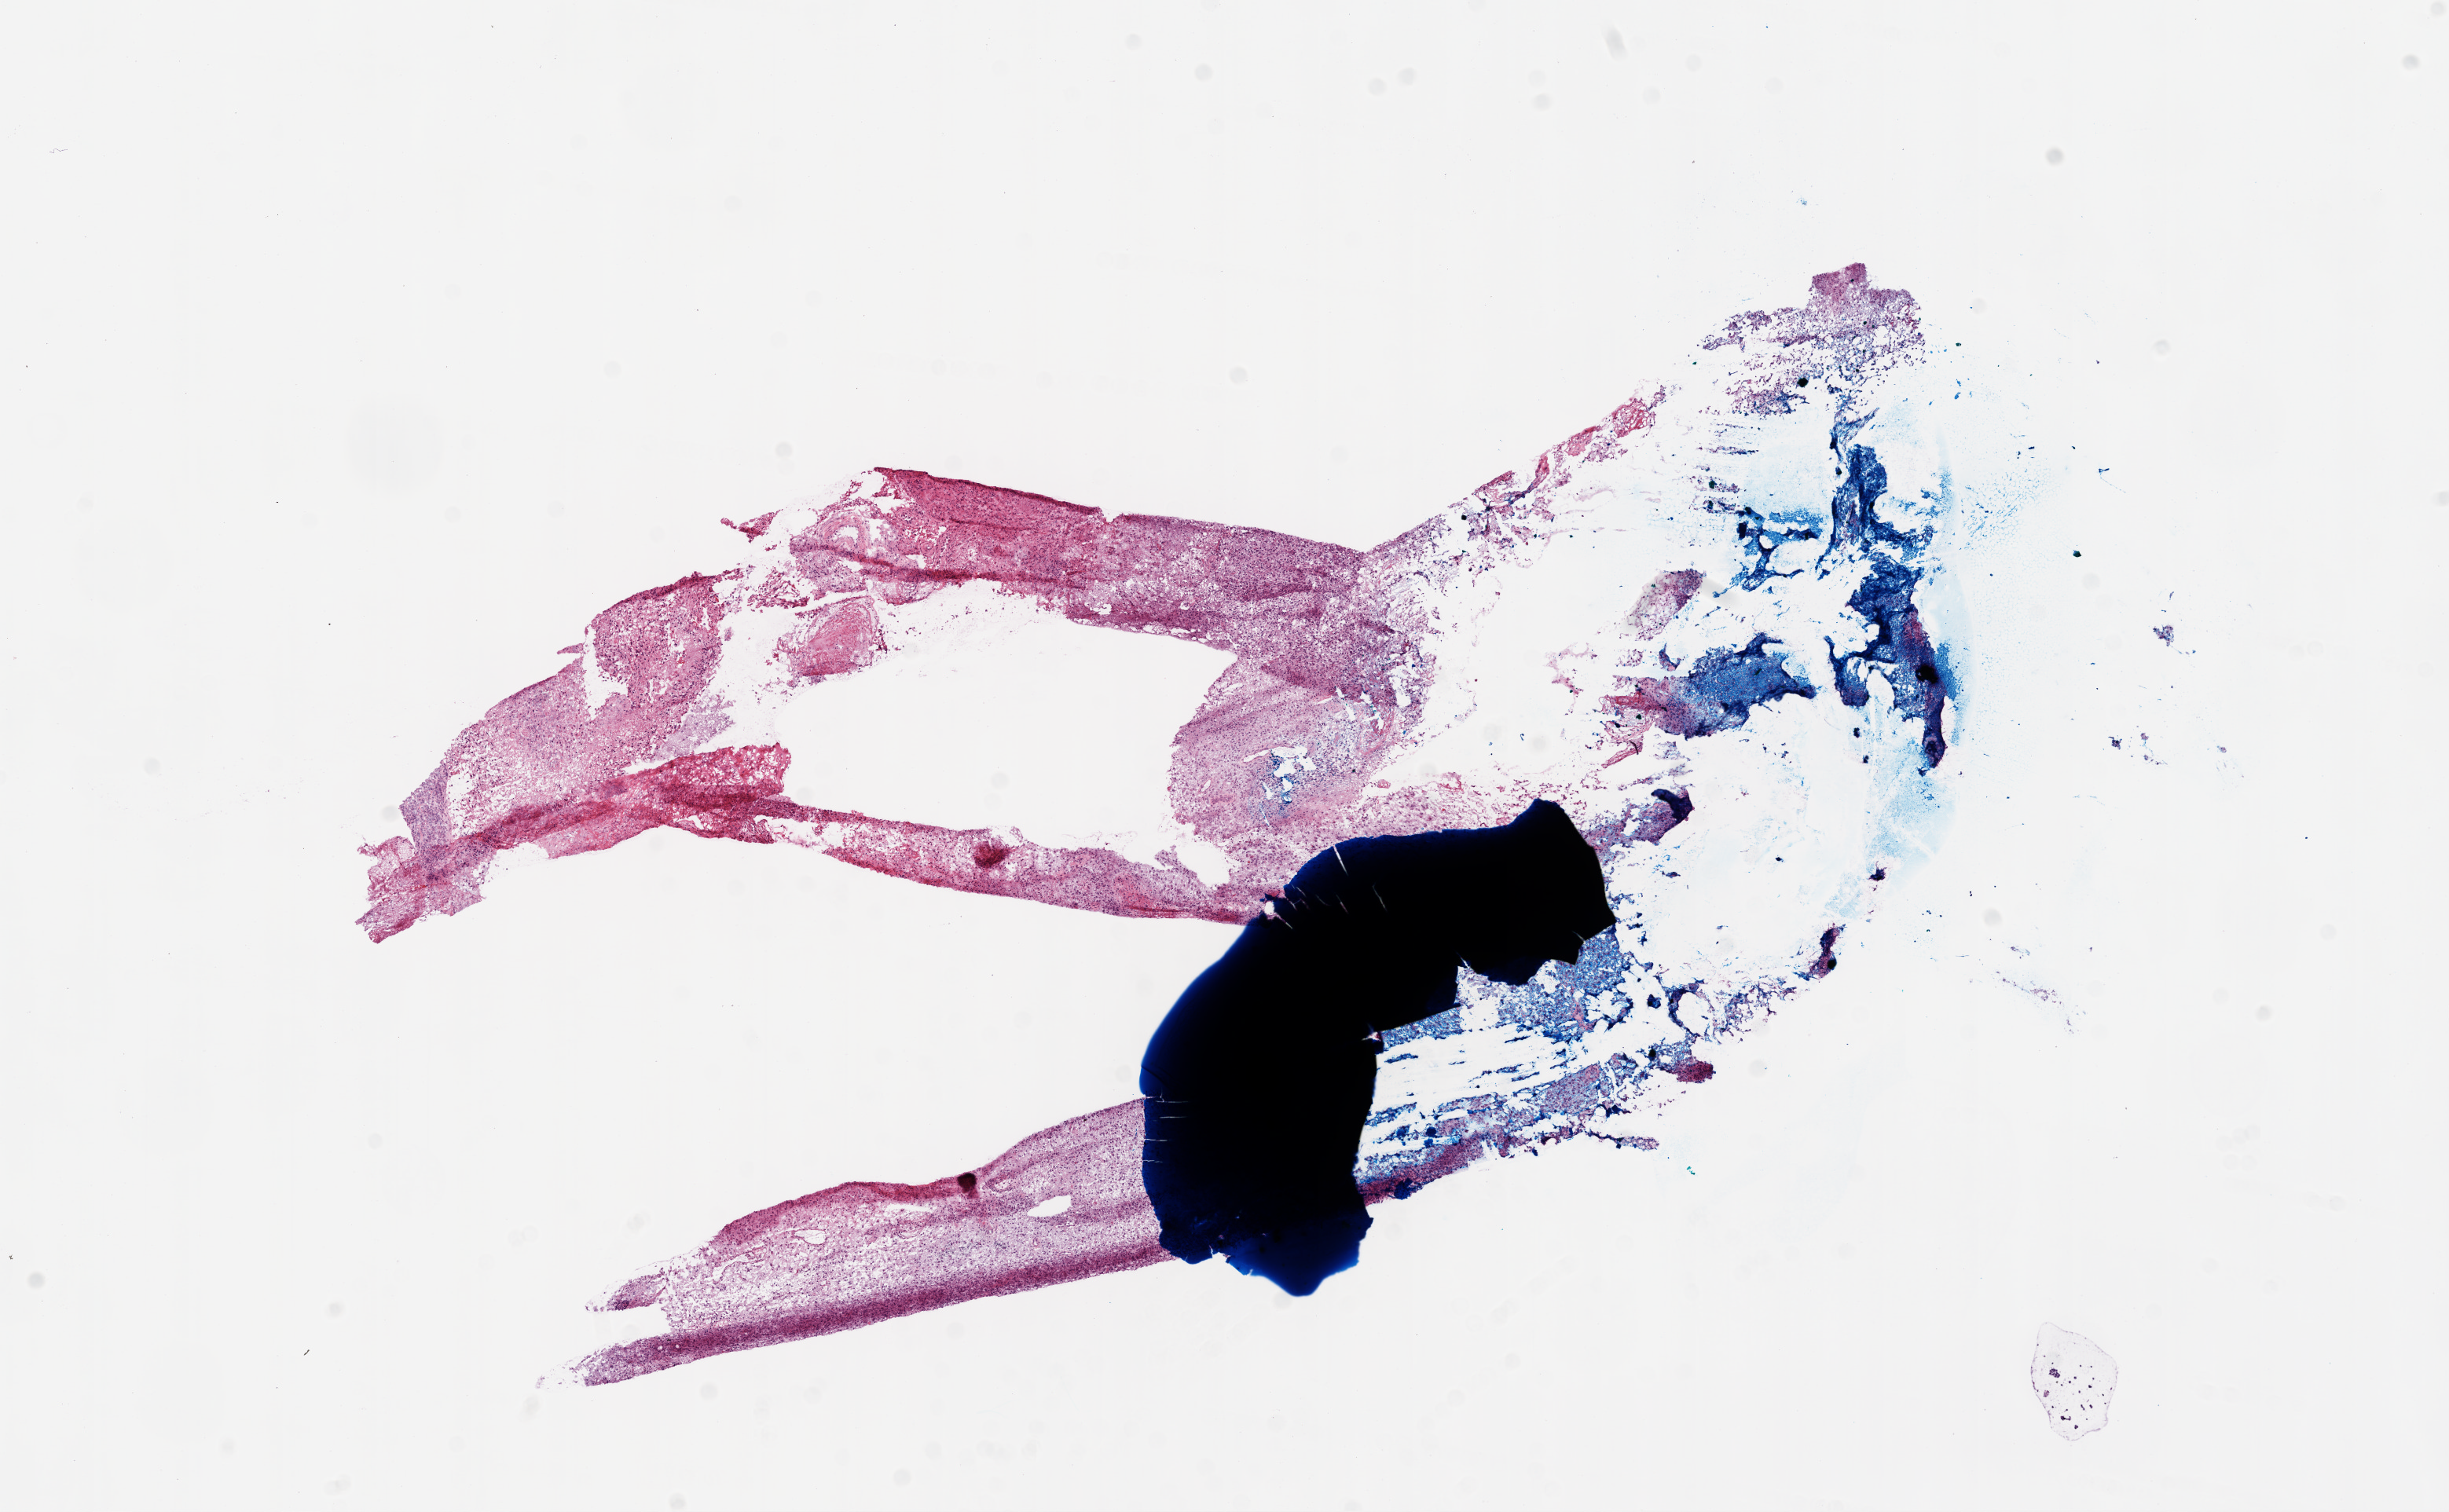
Digitized Hematoxylin and eosin (H&E) stained tissue section (whole slide), shown as a low-resolution overview of the whole scanned area (about 12.6 x 7.8 mm), frozen section from the top of the tissue portion, brain, primary tumour sample. Patient: female, age at initial diagnosis 55 years. Slide review estimates, as recorded: tumour cells 80%, tumour nuclei 100%, normal cells 0%, stromal cells 0%, necrosis 20%.
Diagnosis: Glioblastoma.